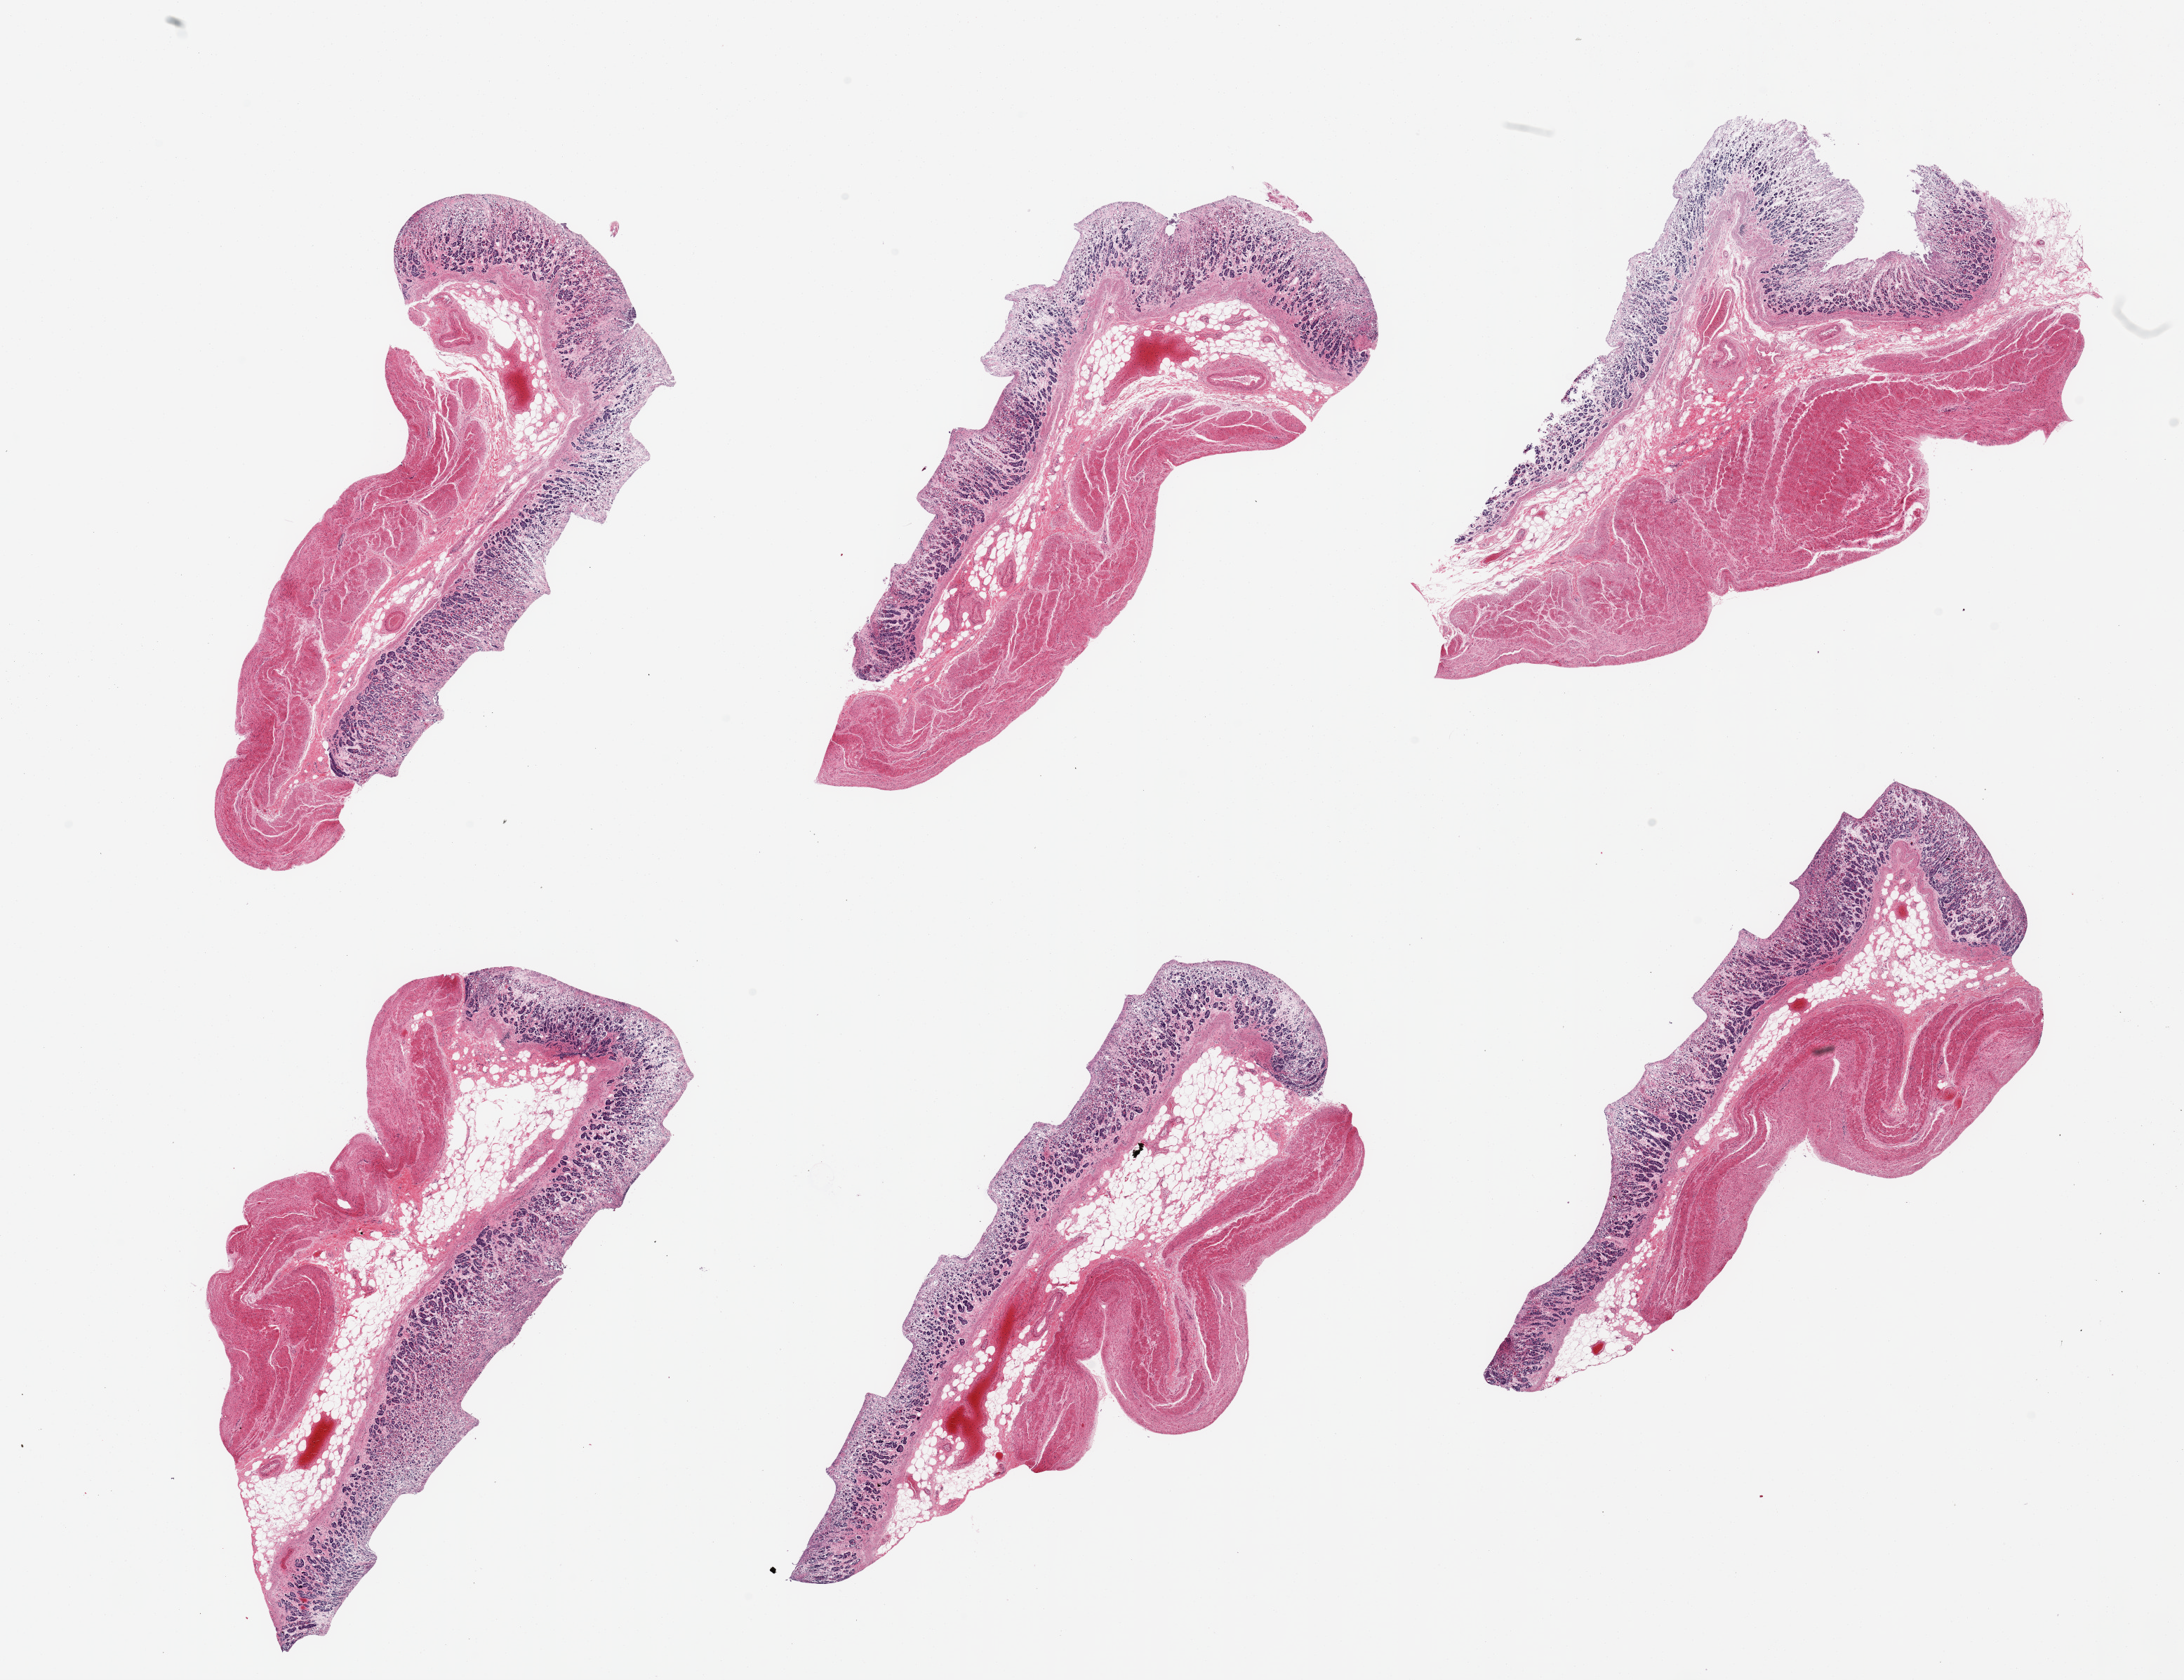
Digitized haematoxylin and eosin-stained section — whole scanned area (about 24.6 x 18.9 mm, slide scanned at 20x) shown as a low-resolution overview; PAXgene-fixed, paraffin-embedded tissue; sampled site (target tissue): stomach; tissue donor sample. Female donor.
Review note (as recorded): 6 pieces, autolyzed mucosa up to ~1mm, ~30% of thickness, glandular mucosa largely degraded.